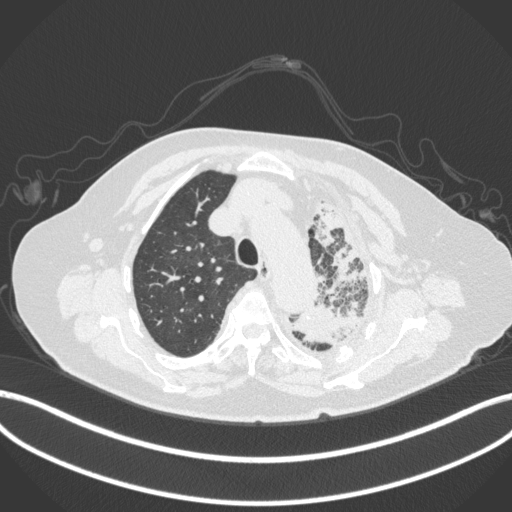
Chest CT, one axial slice. Position 303 of 399 along the scan axis. 120 kVp. Lung window (W 1500 / L -600 HU). 512 × 512 image matrix. Female patient, age 75 years. From the clinical record (not read from this slice): clinical TNM (as recorded): T3 N3 M1.
Annotated regions visible in this slice (rectangle marked by the reading radiologist):
- lung tumour (recorded histology: adenocarcinoma): bounding box (x1, y1, x2, y2) in pixels: (283, 300, 358, 346)